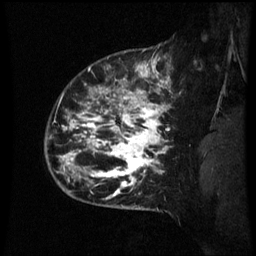
Breast MRI (dynamic contrast-enhanced), one sagittal slice; slice 52 of 60 in the series (ordered by position); dynamic contrast-enhanced series, image 2 of 3 at this slice position (ordered by acquisition); 1.5 T; TE 4.2 ms, TR 8.9 ms; 2.1 mm slice thickness; 256 × 256 image matrix. Female patient, age 42 years. From the clinical record (not read from this slice): setting: breast cancer imaged before/during neoadjuvant chemotherapy; receptor status: HER2-positive.
Annotated regions visible in this slice (semi-automatically segmented with operator editing):
- analysis volume of interest (the breast-tissue region the enhancement analysis was run in; not a lesion): bounding box (x1, y1, x2, y2) in pixels: (66, 82, 171, 193)
- tumour enhancement mask (voxels above the 70 % enhancement threshold inside the analysis volume of interest): (66, 88, 169, 193)